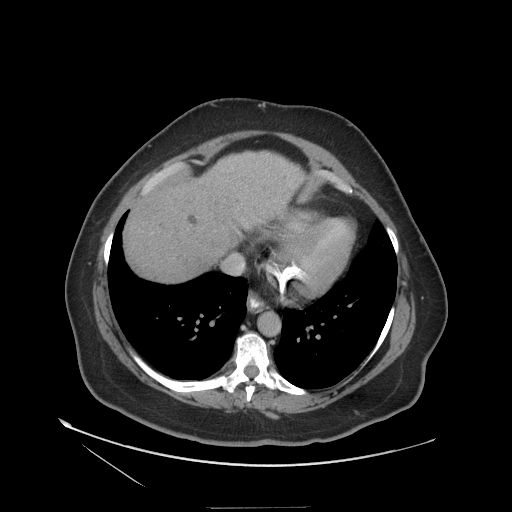
Contrast-enhanced abdominal CT (liver protocol), one axial slice. Slice 104 of 127 in the series (ordered by position). Reconstruction kernel STANDARD. Soft-tissue window (W 400 / L 40 HU). 512 × 512 image matrix, field of view 480 × 480 mm. From the clinical record (not read from this slice): diagnosis: hepatocellular carcinoma (patient treated with transarterial chemoembolisation; whether this scan precedes or follows treatment is not stated here); TNM stage (as recorded): Stage-II; Child-Pugh class: A; tumour differentiation: well differentiated; tumour size: 3 cm.
Outlined on this slice (semi-automatically segmented with operator editing):
- liver parenchyma outside the tumour (the mass and vessels are separate outlines, so this box may not span the whole liver): bounding box (x1, y1, x2, y2) in pixels: (124, 152, 303, 280)
- liver vessels: (145, 169, 171, 193)